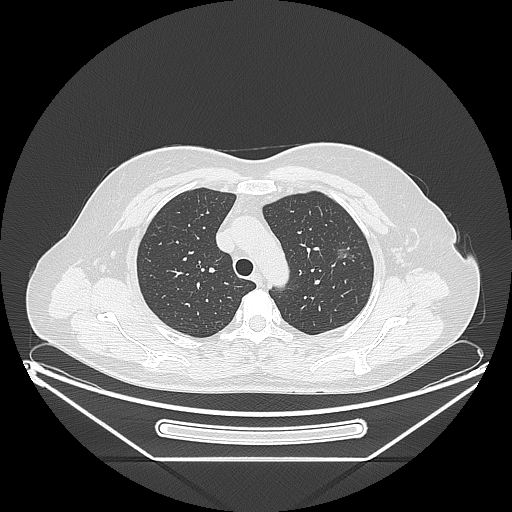
Chest CT, one axial slice. Slice 167 of 226 in the series (ordered by position). Reconstruction kernel LUNG. 120 kVp. Lung window (W 1500 / L -600 HU). 512 × 512 image matrix, field of view 447 × 447 mm. Female patient, age 54 years. Case-level facts recorded for this patient, not image findings: clinical TNM (as recorded): T1c N0 M0.
Structures marked on this image (rectangle marked by the reading radiologist):
- lung tumour (recorded histology: adenocarcinoma): bounding box (x1, y1, x2, y2) in pixels: (333, 240, 362, 271)